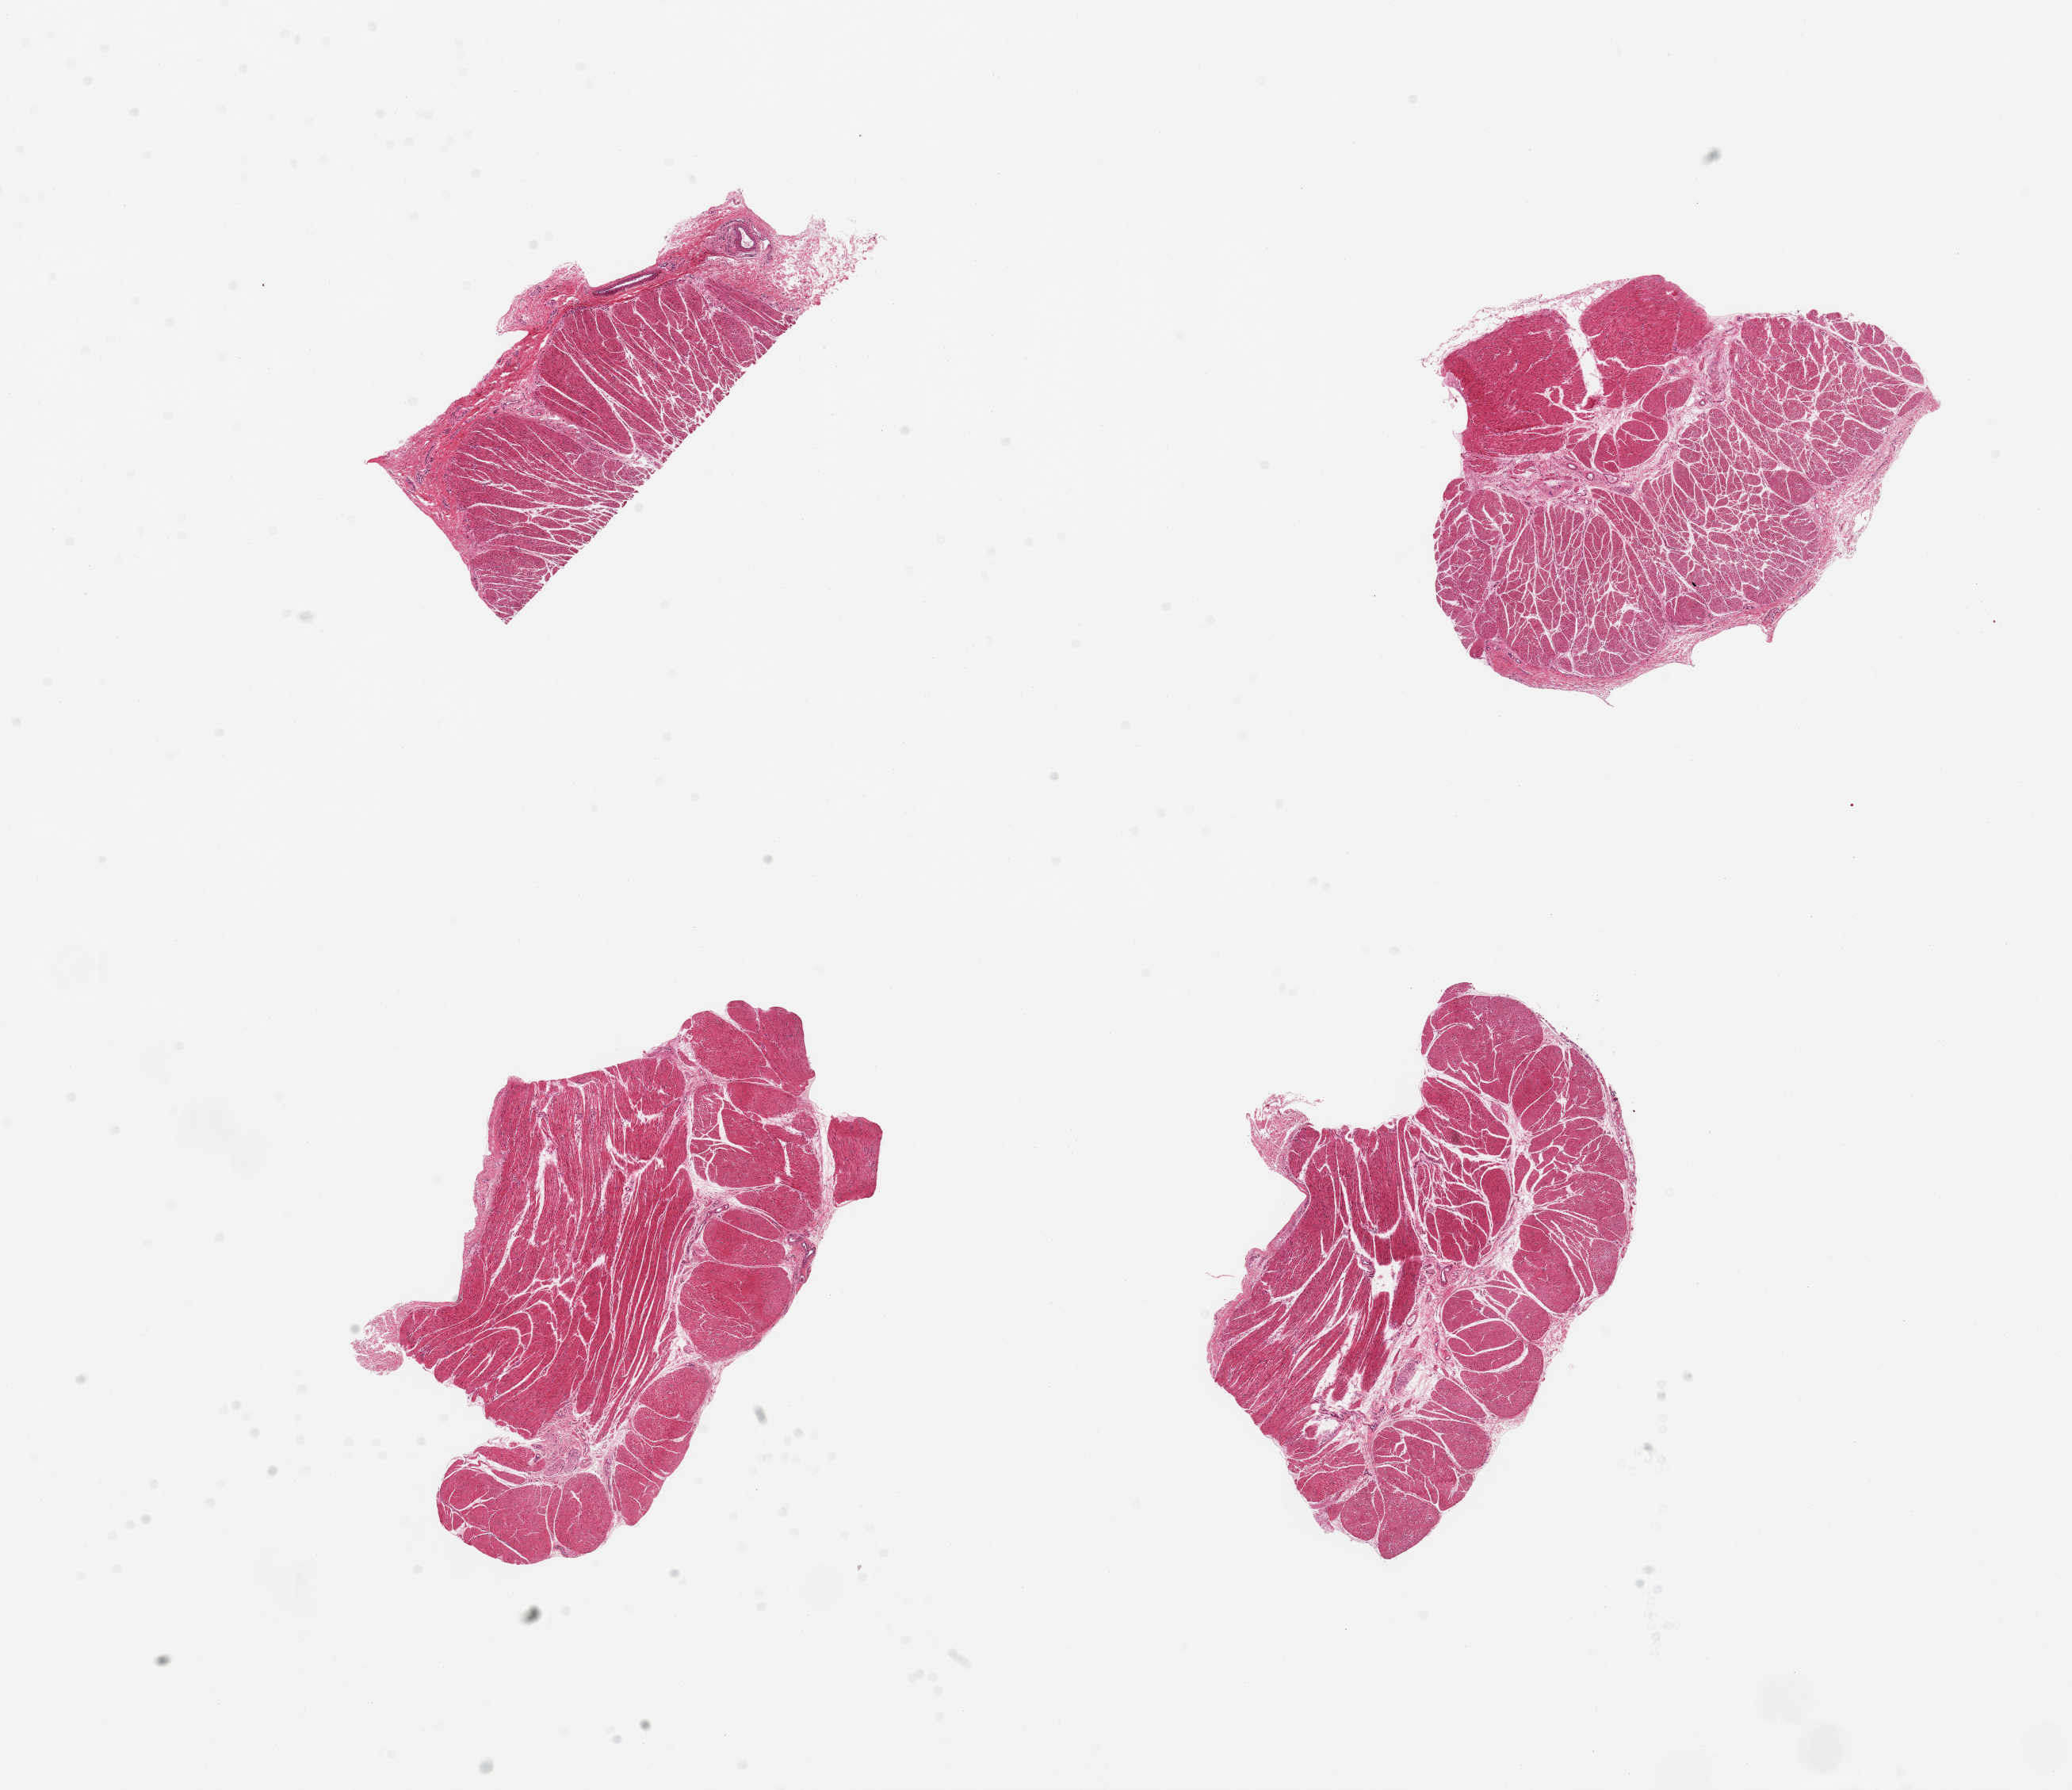
Whole-slide image, haematoxylin and eosin stain, brightfield, low-resolution overview of the scanned area, about 20.7 x 17.9 mm, PAXgene-fixed, paraffin-embedded tissue, target tissue: esophageal muscle, tissue donor sample. Male donor.
- reviewer comment on this tissue sample: 4 pieces, confirmed target muscularis